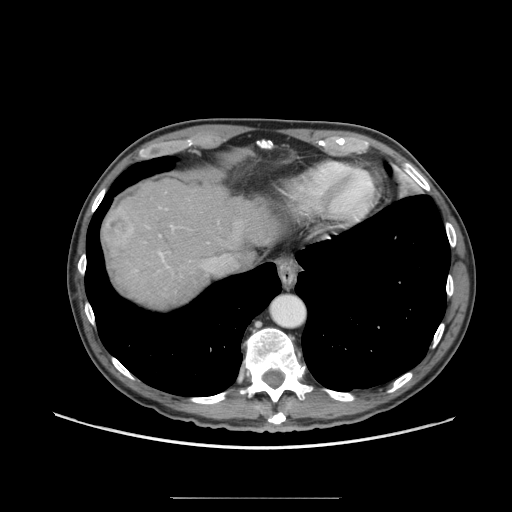
Contrast-enhanced abdominal CT (liver protocol), one axial slice; position 58 of 71 along the scan axis; reconstruction kernel STANDARD; soft-tissue window (W 400 / L 40 HU); 512 × 512 image matrix, field of view 400 × 400 mm. From the clinical record (not read from this slice): diagnosis: hepatocellular carcinoma (patient treated with transarterial chemoembolisation; whether this scan precedes or follows treatment is not stated here); TNM stage (as recorded): Stage-I; Child-Pugh class: A; tumour differentiation: well differentiated; tumour nodularity: uninodular.
Outlined on this slice (semi-automatic segmentation, software-assisted and operator-edited):
- abdominal aorta: bounding box [x1, y1, x2, y2] px = [271, 295, 305, 327]
- liver parenchyma outside the tumour (the mass and vessels are separate outlines, so this box may not span the whole liver): [104, 180, 278, 307]
- mass: [103, 208, 136, 248]
- liver vessels: [136, 226, 217, 271]